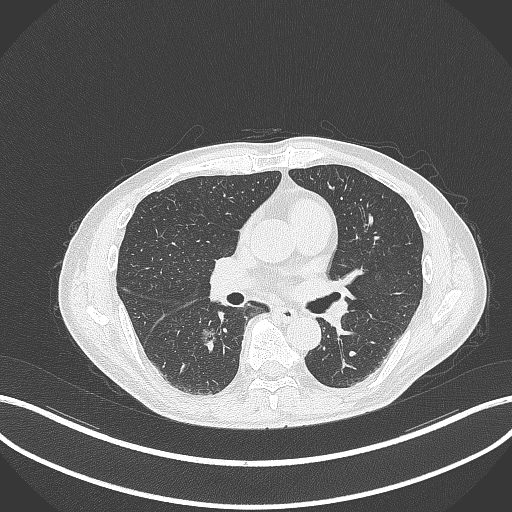
Chest CT, one axial slice. 120 kVp. Lung window (W 1500 / L -600 HU). 1 mm slice thickness. 512 × 512 image matrix. Male patient, age 61 years. From the clinical record (not read from this slice): clinical TNM (as recorded): T1c N0 M0.
Annotated regions visible in this slice (bounding box drawn by a radiologist):
- lung tumour (recorded histology: adenocarcinoma): bounding box [x1, y1, x2, y2] px = [200, 324, 221, 349]